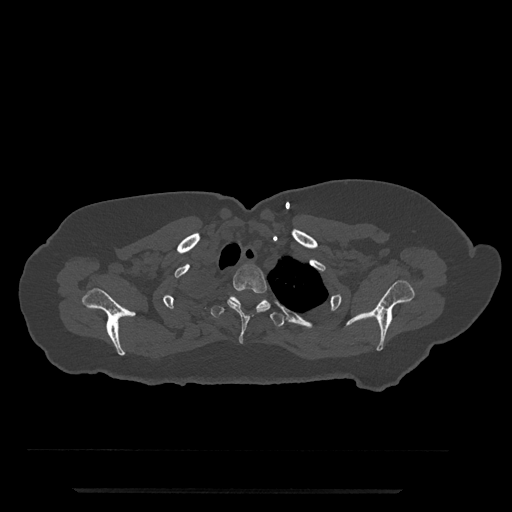
CT including the spine, one axial slice; slice 660 of 797 in the series (ordered by position); reconstruction kernel Br40s/3; bone window (W 1800 / L 400 HU); 0.5 mm slice thickness; 512 × 512 image matrix. Patient: female, 51 years. From the clinical record (not read from this slice): primary cancer: neuro.
Outlined on this slice (semi-automatically segmented with operator editing):
- T2 vertebra: bounding box (x1, y1, x2, y2) in pixels: (227, 264, 270, 343)
- T3 vertebra: (211, 295, 284, 327)